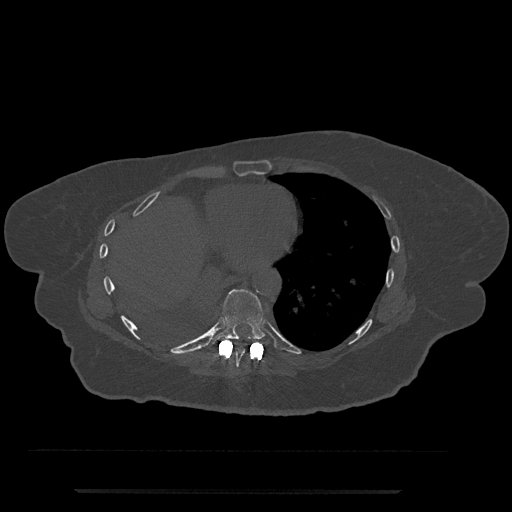
CT including the spine, one axial slice; slice 357 of 797 in the series (ordered by position); reconstruction kernel Br40s/3; 120 kVp; bone window (W 1800 / L 400 HU); 512 × 512 image matrix, field of view 440 × 440 mm. Female patient, age 51 years. Case-level facts recorded for this patient, not image findings: primary cancer: neuro; vertebrae with lytic lesions (as recorded): T8.
Outlined on this slice (semi-automatically segmented with operator editing):
- T8 vertebra: bounding box (x1, y1, x2, y2) in pixels: (230, 347, 246, 370)
- T9 vertebra: (209, 289, 271, 347)